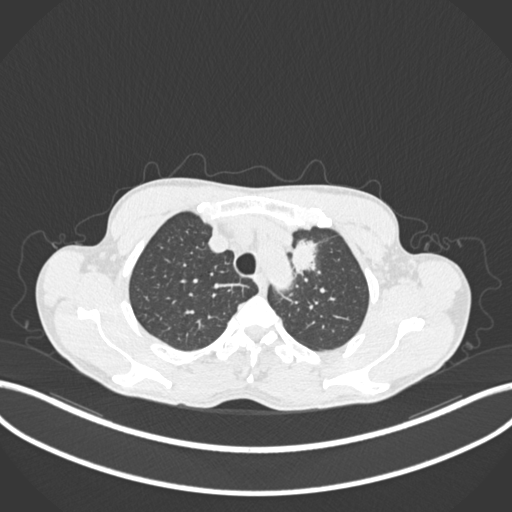
Chest CT, one axial slice; slice 166 of 211 in the series (ordered by position); reconstruction kernel B30f; lung window (W 1500 / L -600 HU); 1 mm slice thickness; 512 × 512 image matrix. Patient: male, 58 years. From the clinical record (not read from this slice): clinical TNM (as recorded): T1c N1 M0.
Structures marked on this image (bounding box drawn by a radiologist):
- lung tumour (recorded histology: adenocarcinoma): bounding box (x1, y1, x2, y2) in pixels: (289, 236, 327, 286)